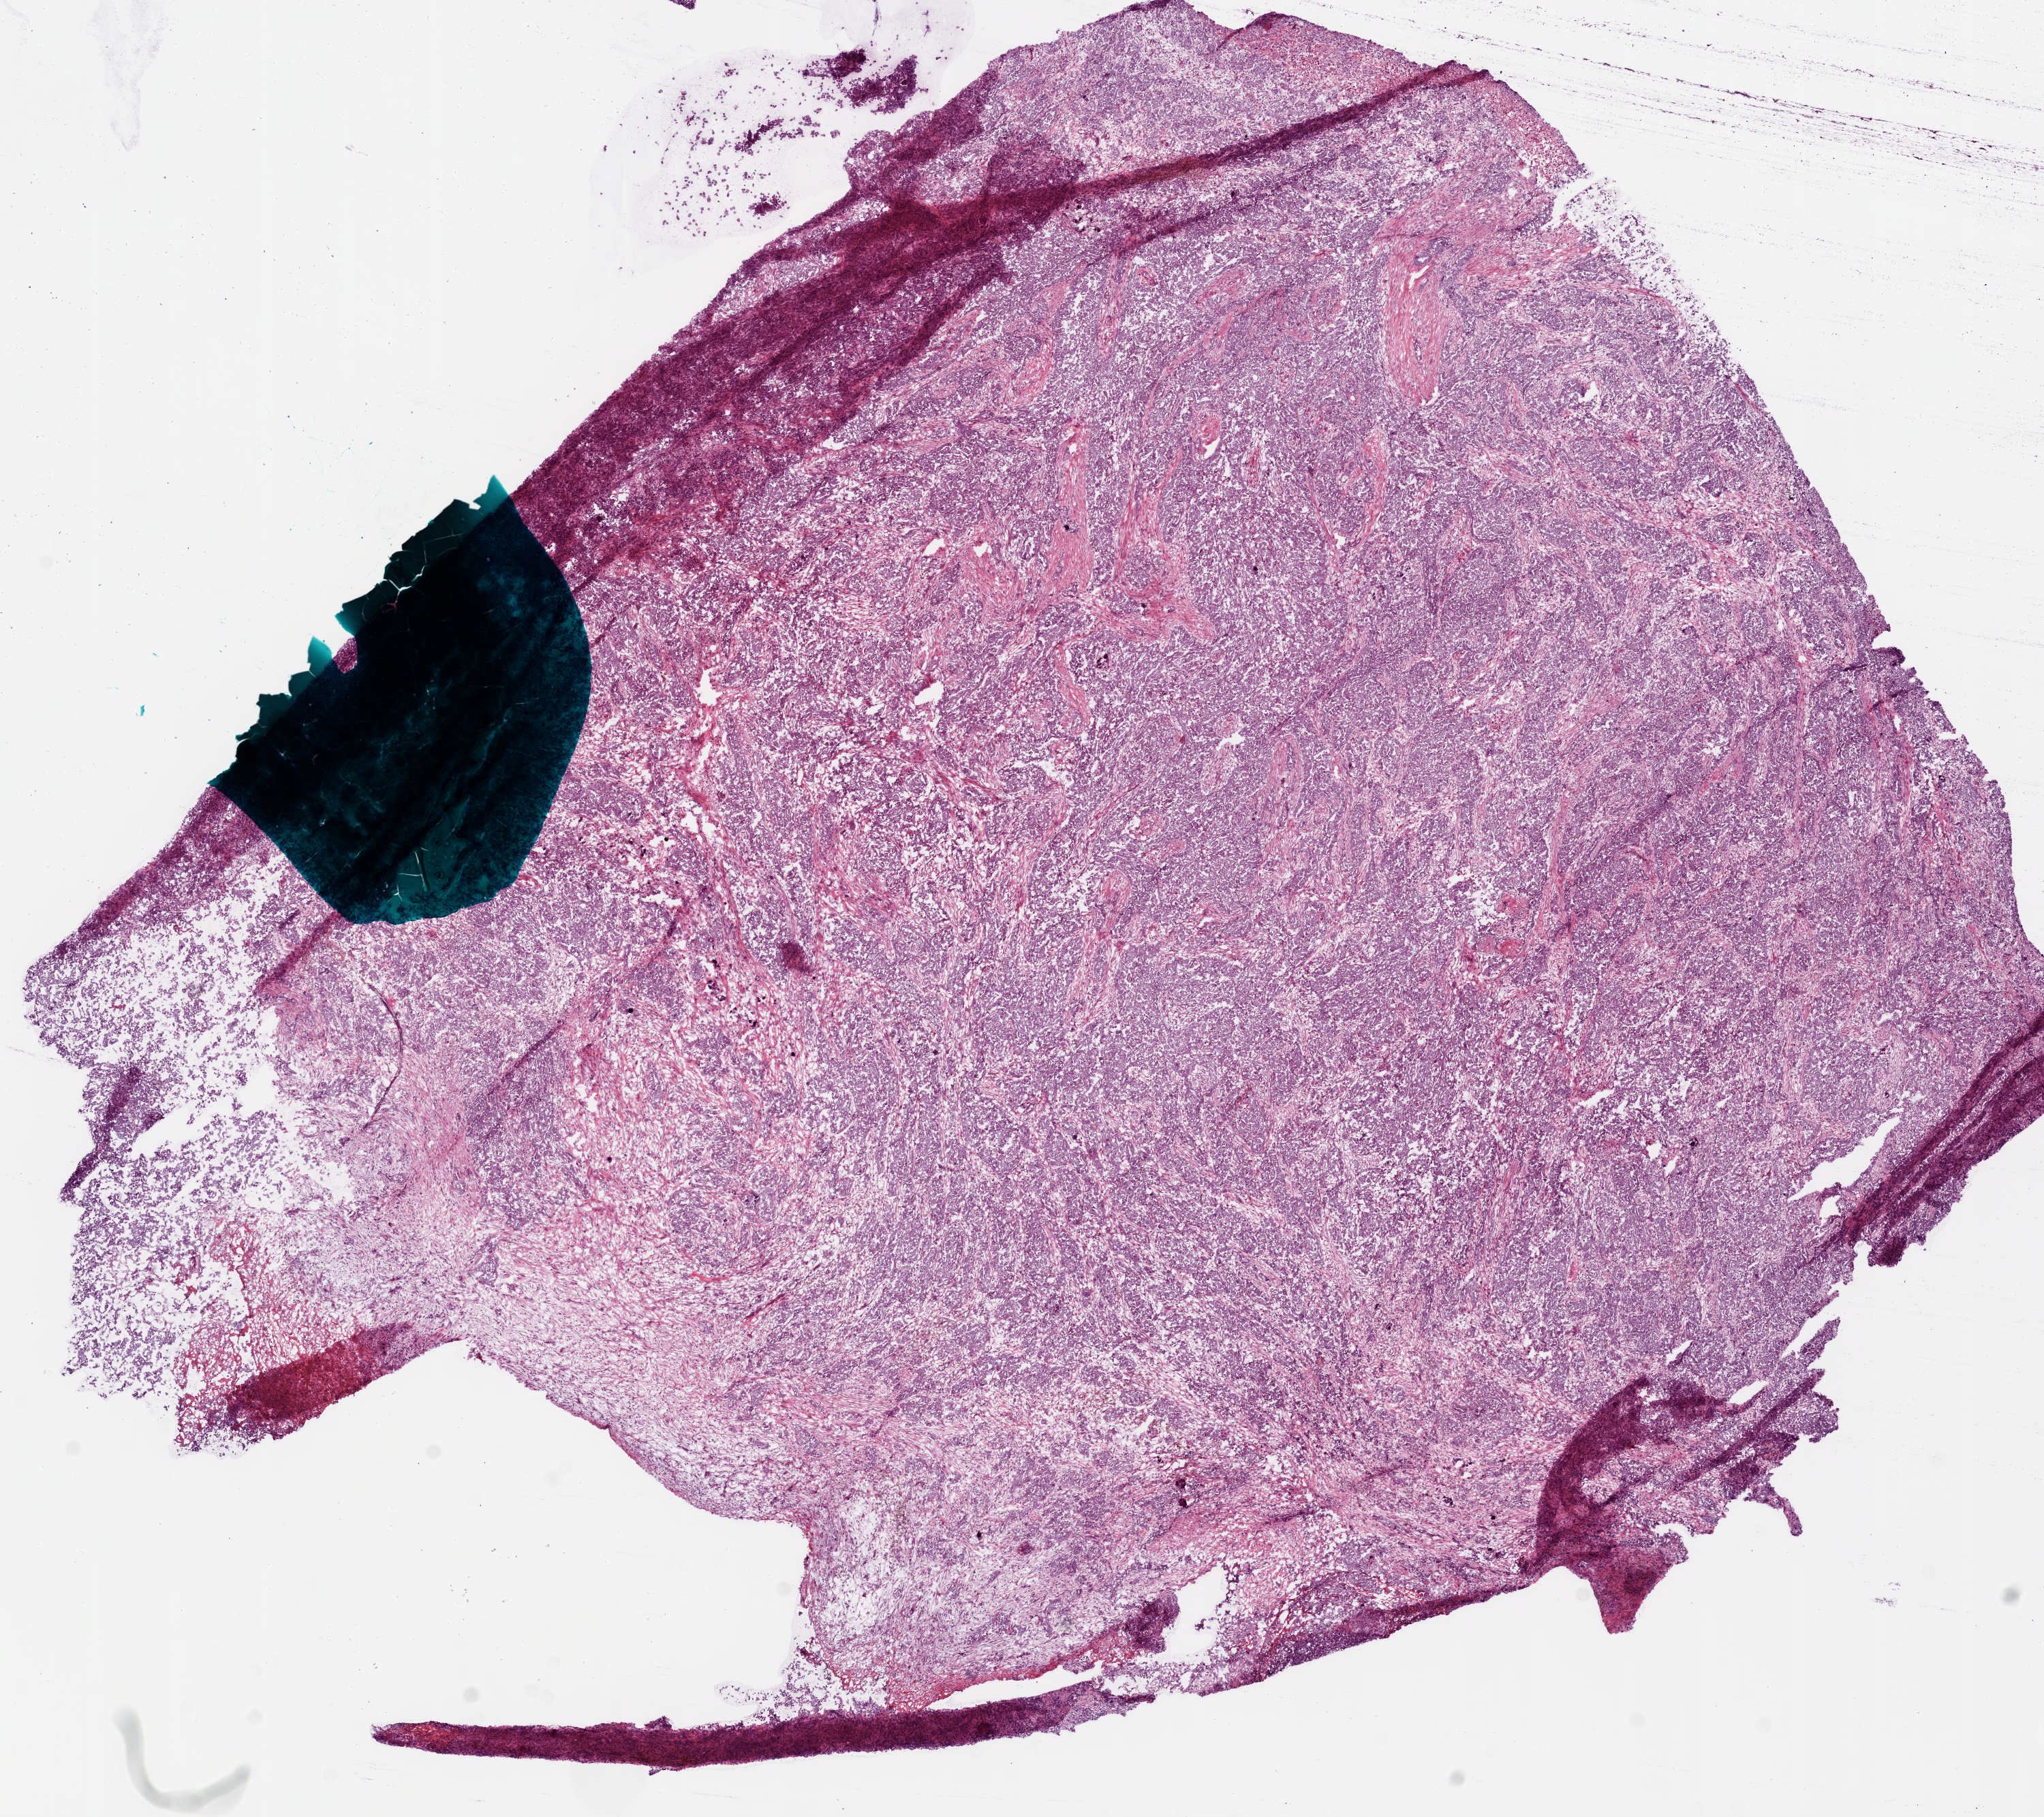
Digitized Hematoxylin and eosin (H&E) stained tissue section (whole slide), low-resolution overview of the scanned area, about 12.0 x 10.7 mm, frozen section from the bottom of the tissue portion, primary tumour sample from the ovary. Female patient; age at initial diagnosis 82 years.
Pathologic diagnosis: Serous cystadenocarcinoma, NOS.